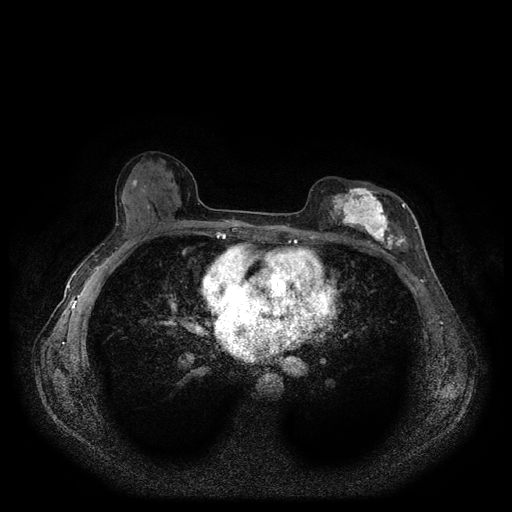
Breast MRI (dynamic contrast-enhanced, multi-phase), one axial slice. Slice 55 of 116 in the series (ordered by position). Dynamic contrast-enhanced series, time point 2 of 5 at this slice position (early post-contrast). 1.5 T. TE 2.6 ms, TR 5.3 ms. 2 mm slice thickness. 512 × 512 image matrix, field of view 350 × 350 mm. Patient: female, 51 years.
Structures marked on this image (semi-automatically segmented with operator editing):
- breast lesion (labelled 'tumour' in the annotation; benign lesions carry a separate 'benign' label): bounding box [x1, y1, x2, y2] px = [323, 186, 411, 255]